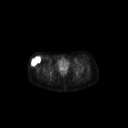
FDG PET of an extremity soft-tissue mass (from a PET/CT study), one axial slice. Position 60 of 267 along the scan axis. 3.27 mm slice thickness. 128 × 128 image matrix. Patient: female, 34 years. Case-level facts recorded for this patient, not image findings: histological type: synovial sarcoma; grade: intermediate; site of the primary tumour: right thigh.
Annotated regions visible in this slice (expert contour drawn on MRI and transferred to this co-registered scan by the dataset authors):
- gross tumour volume including surrounding oedema: box from (x=30, y=56) to (x=40, y=67) px
- gross tumour volume (mass): (x=30, y=56)–(x=40, y=67)